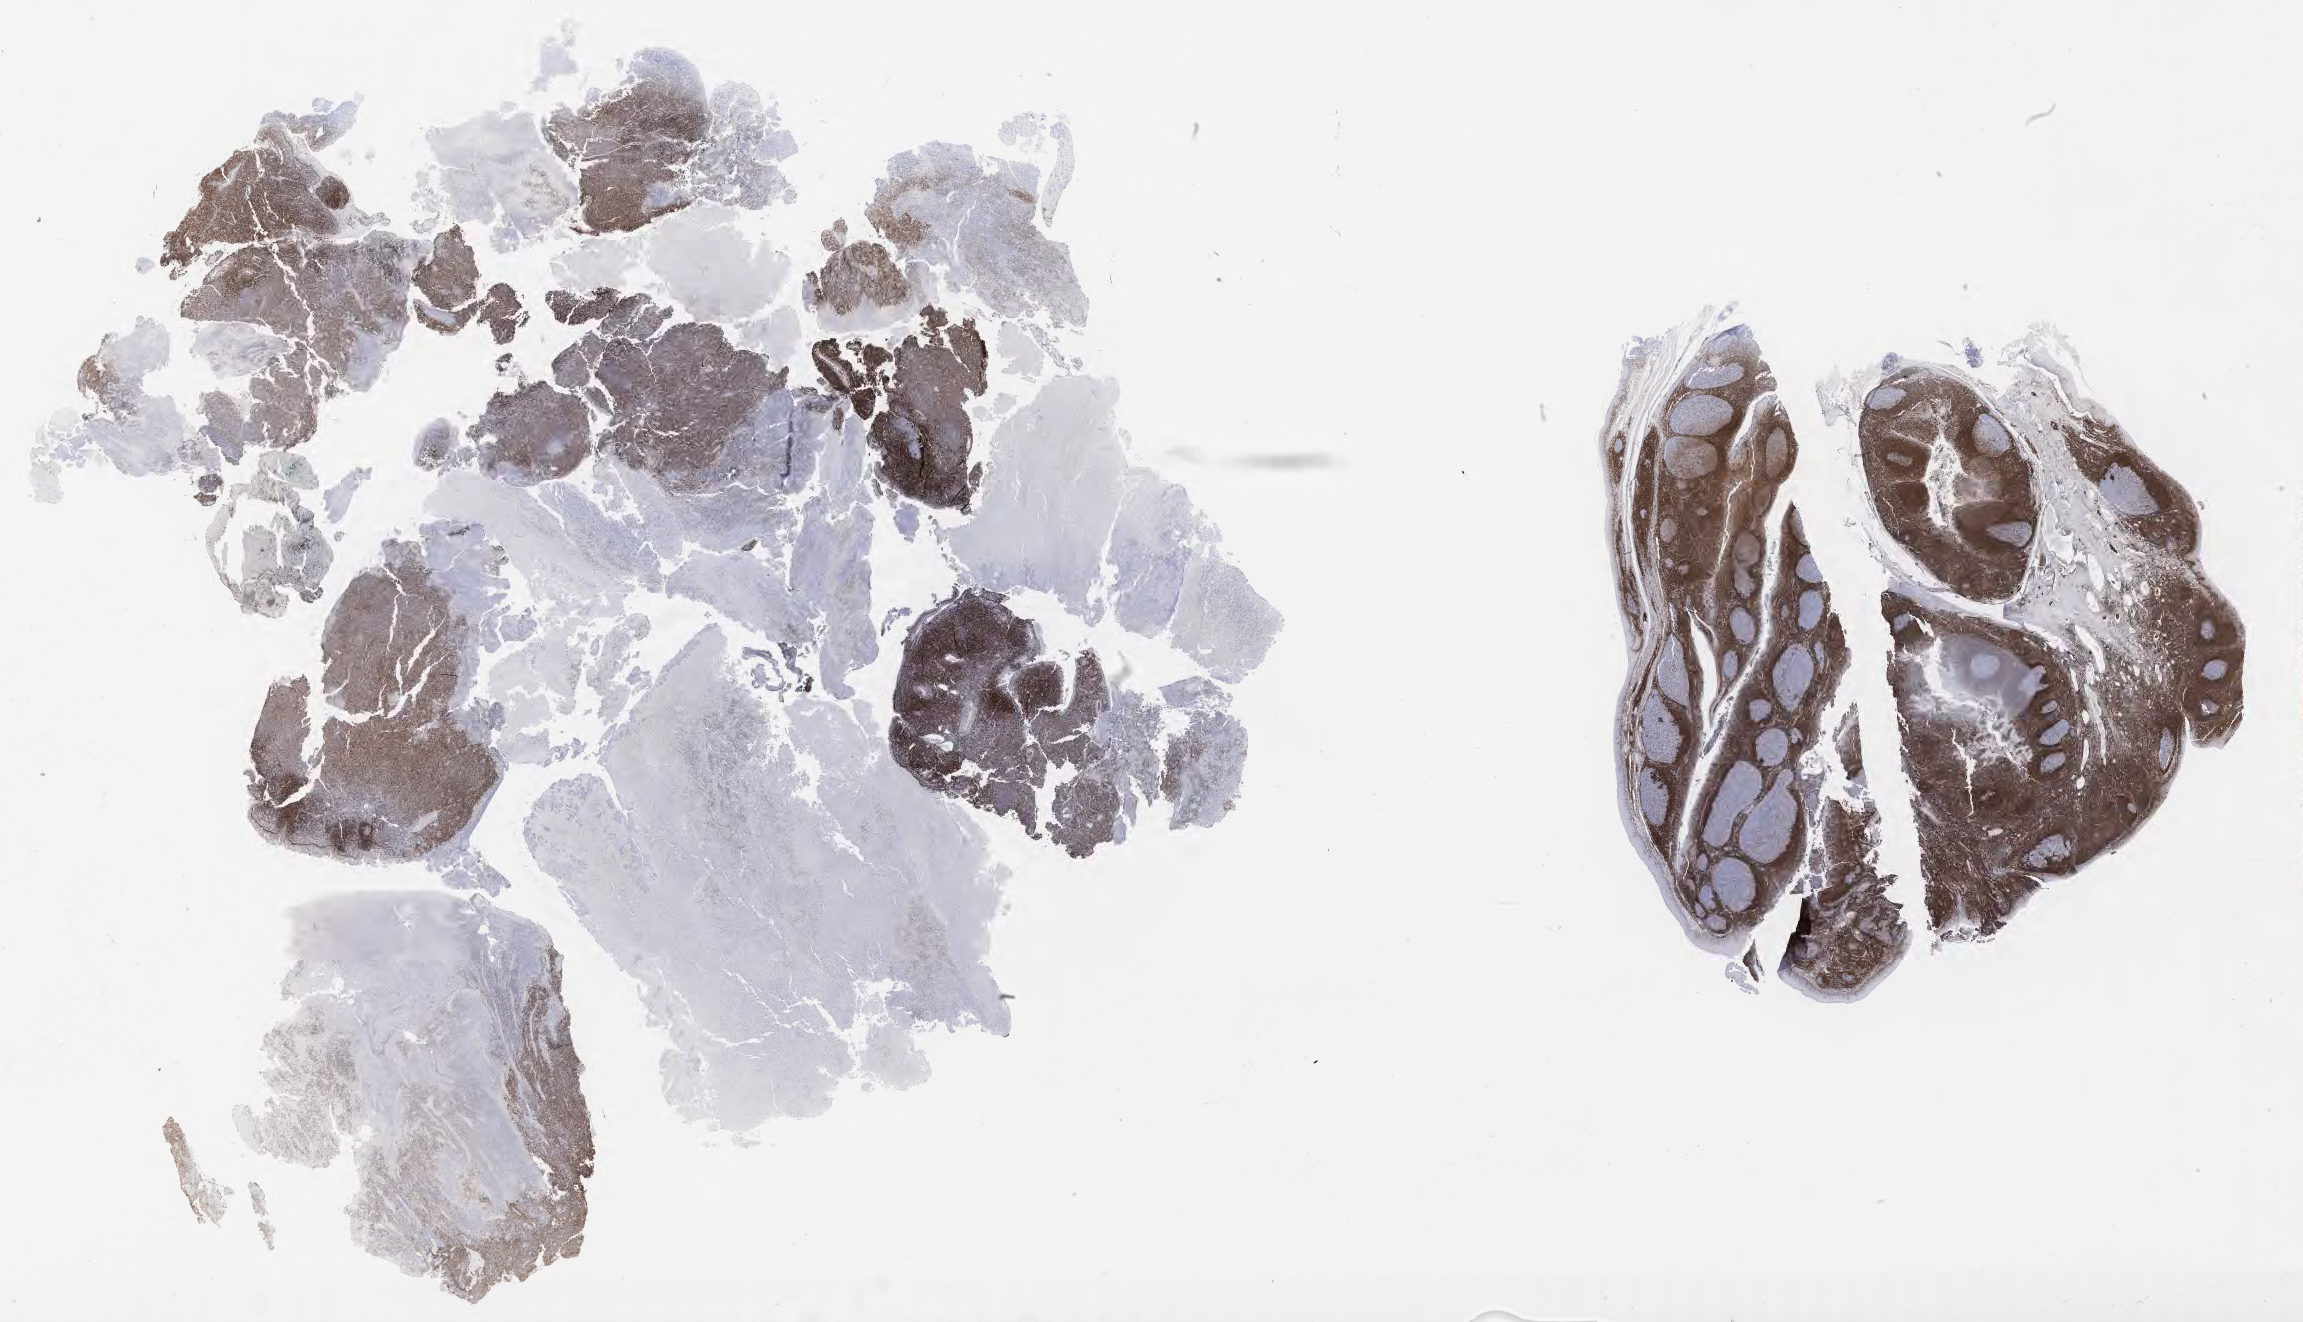
Immunohistochemistry (IHC) whole-slide image stained for BCL2 — whole scanned area (about 37.2 x 21.4 mm) shown as a low-resolution overview, tumor tissue. Male patient, age 47 years.
Histologic diagnosis: Diffuse large B-cell lymphoma, NOS.